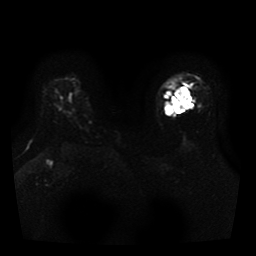
Breast MRI, one axial slice. Slice 30 of 41 in the series (ordered by position). Diffusion-weighted series; image 2 of 3 stored at this slice position (different b-values; order by instance number). 1.5 T. 5 mm slice thickness. 256 × 256 image matrix, field of view 330 × 330 mm. Female patient.
Structures marked on this image (outlined manually by an expert reader):
- tumour on diffusion-weighted imaging: bounding box (x1, y1, x2, y2) in pixels: (165, 97, 189, 114)